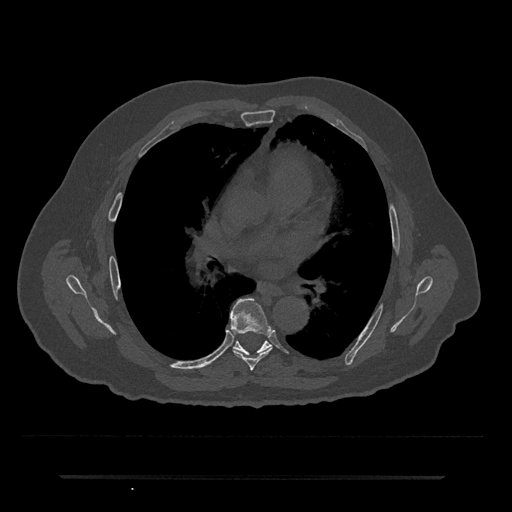
CT including the spine, one axial slice. Position 417 of 797 along the scan axis. Reconstruction kernel Br40s/3. Bone window (W 1800 / L 400 HU). 0.5 mm slice thickness. 512 × 512 image matrix. Patient: male, 69 years. From the clinical record (not read from this slice): primary cancer: prostate.
Outlined on this slice (semi-automatically segmented with operator editing):
- T6 vertebra: bounding box <230,299,274,371> (left, top, right, bottom; pixels)
- T7 vertebra: <233,341,271,355>